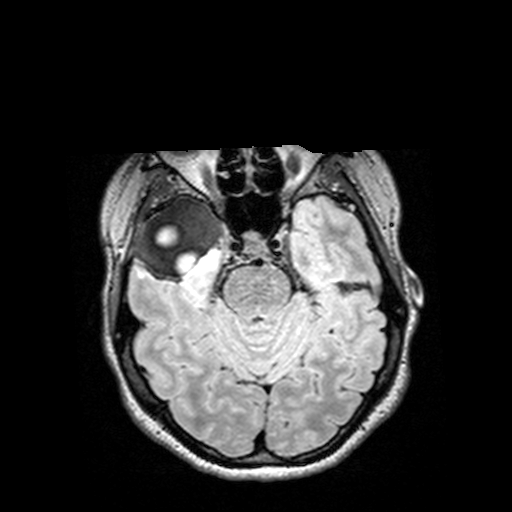
Brain MRI from a brain-tumour surgery series, one axial slice. Position 98 of 144 along the scan axis. T2 FLAIR. 1 mm slice thickness. 512 × 512 image matrix, field of view 250 × 250 mm. From the clinical record (not read from this slice): histopathology: Astrocytoma; WHO grade: 3; IDH mutation: yes.
Outlined on this slice (manually delineated by an expert):
- tumour: bounding box [x1, y1, x2, y2] px = [126, 196, 232, 284]